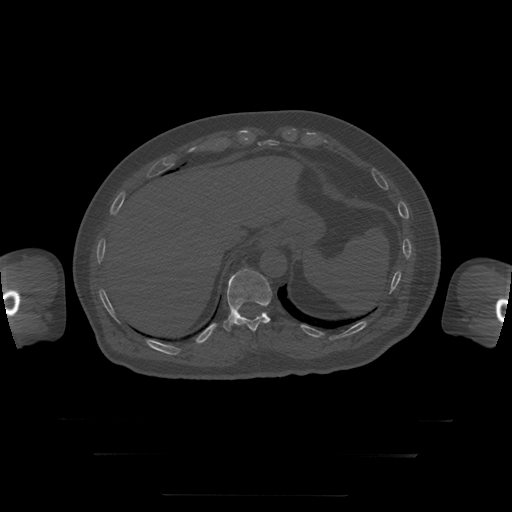
CT including the spine, one axial slice. Position 100 of 397 along the scan axis. Reconstruction kernel STANDARD. 120 kVp. Bone window (W 1800 / L 400 HU). 1.25 mm slice thickness. 512 × 512 image matrix, field of view 510 × 510 mm. Patient age 73 years. From the clinical record (not read from this slice): primary cancer: prostate.
Outlined on this slice (semi-automatically segmented with operator editing):
- T11 vertebra: bounding box (x1, y1, x2, y2) in pixels: (223, 269, 272, 332)